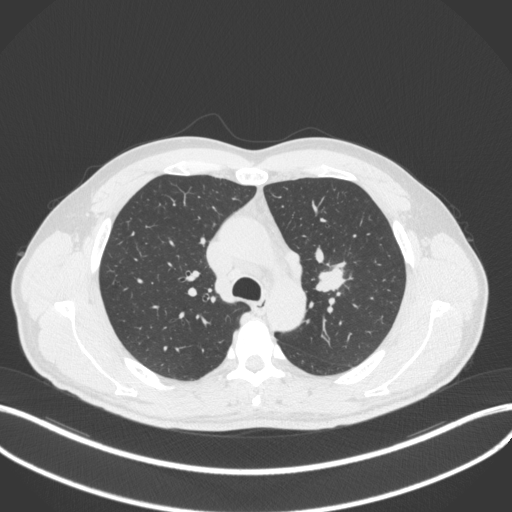
Chest CT, one axial slice; slice 295 of 383 in the series (ordered by position); reconstruction kernel B31f; lung window (W 1500 / L -600 HU); 512 × 512 image matrix, field of view 400 × 400 mm. Male patient, age 50 years. Case-level facts recorded for this patient, not image findings: clinical TNM (as recorded): T1c N1 M1b.
Structures marked on this image (rectangle marked by the reading radiologist):
- lung tumour (recorded histology: squamous cell carcinoma): bounding box (x1, y1, x2, y2) in pixels: (316, 265, 348, 296)